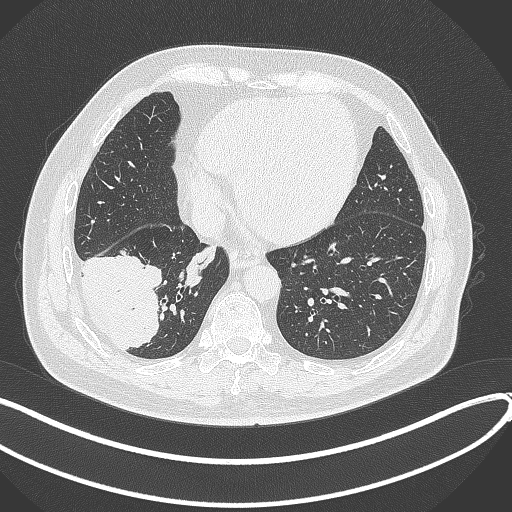
Chest CT, one axial slice; position 109 of 360 along the scan axis; reconstruction kernel B70f; 120 kVp; lung window (W 1500 / L -600 HU); 1 mm slice thickness; 512 × 512 image matrix, field of view 400 × 400 mm. Patient: male, 59 years.
Structures marked on this image (bounding box drawn by a radiologist):
- lung tumour (recorded histology: adenocarcinoma): bounding box (x1, y1, x2, y2) in pixels: (77, 249, 164, 352)